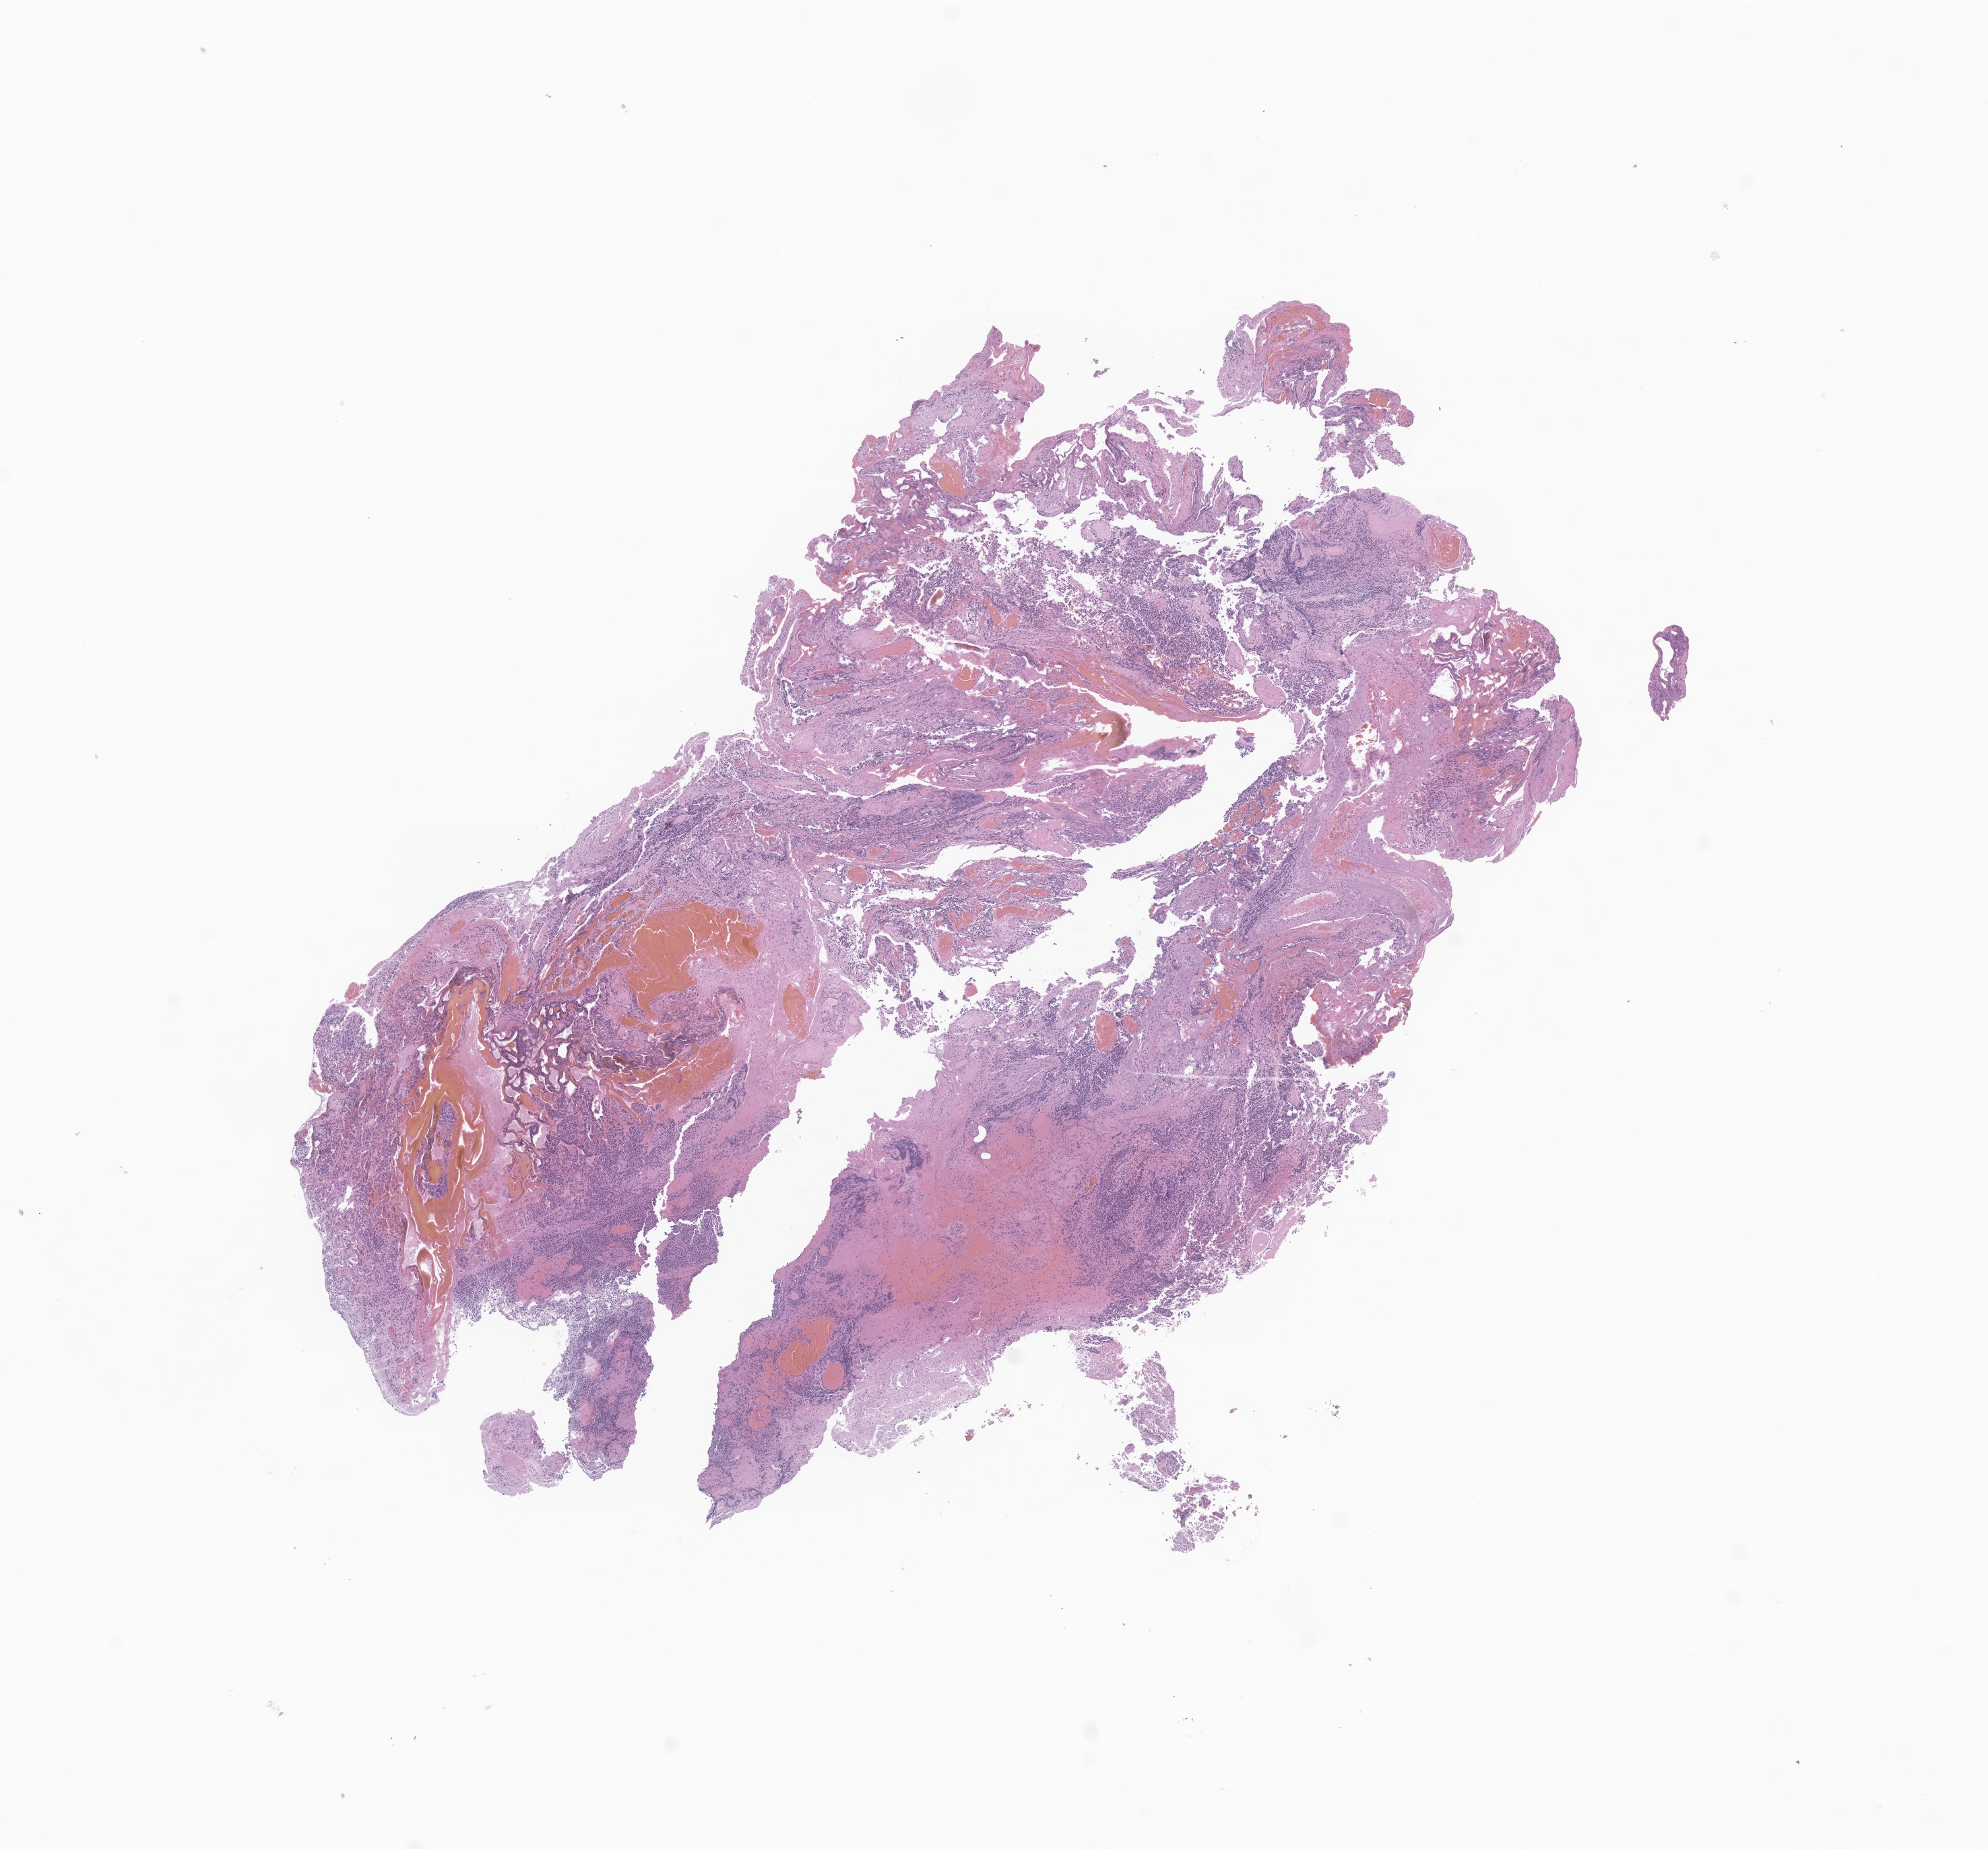
H&E whole-slide image of tumor tissue from the cerebral ventricle — shown as a low-resolution overview of the whole scanned area (about 12.4 x 11.6 mm), formalin-fixed, paraffin-embedded (FFPE) tissue. Patient: male, age 64 months (5 years 4 months).
• diagnosis (ICD-O-3 morphology term): Medulloblastoma, NOS